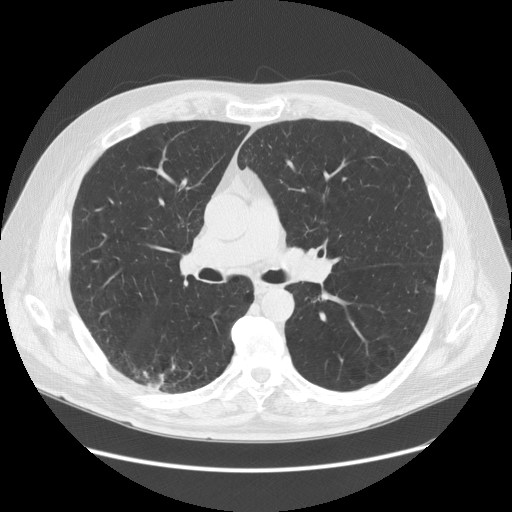
Low-dose screening chest CT, one axial slice; position 85 of 149 along the scan axis; 120 kVp; lung window (W 1500 / L -600 HU); 512 × 512 image matrix, field of view 400 × 400 mm.
Structures marked on this image (expert manual segmentation):
- lesion 1 (tumor, lower lobe of right lung): bounding box <143,371,166,390> (left, top, right, bottom; pixels)